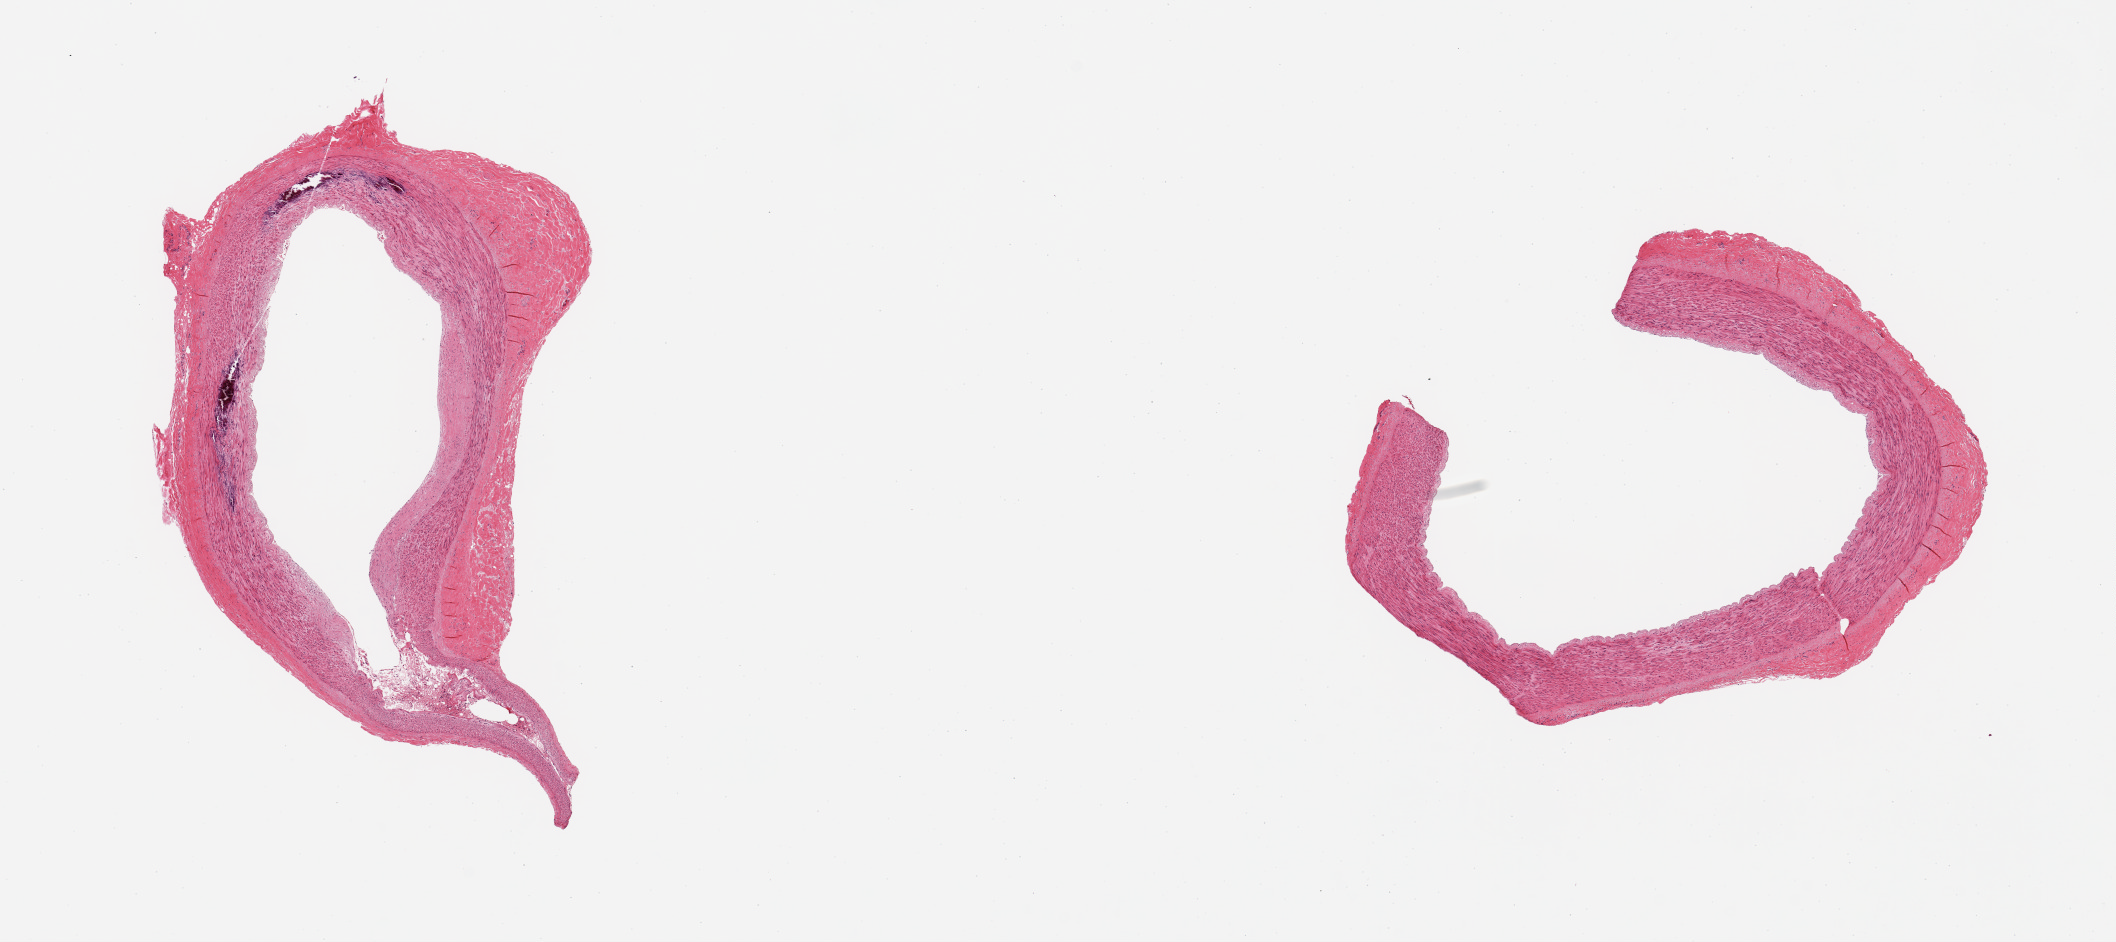
Haematoxylin and eosin whole-slide image — a low-resolution overview of the entire scanned area, about 16.7 x 7.5 mm. PAXgene-fixed, paraffin-embedded tissue. Target tissue: tibial artery. Tissue donor sample.
• review note (as recorded): 2 pieces; mild plaque; prominent medial calcium deposits in 1